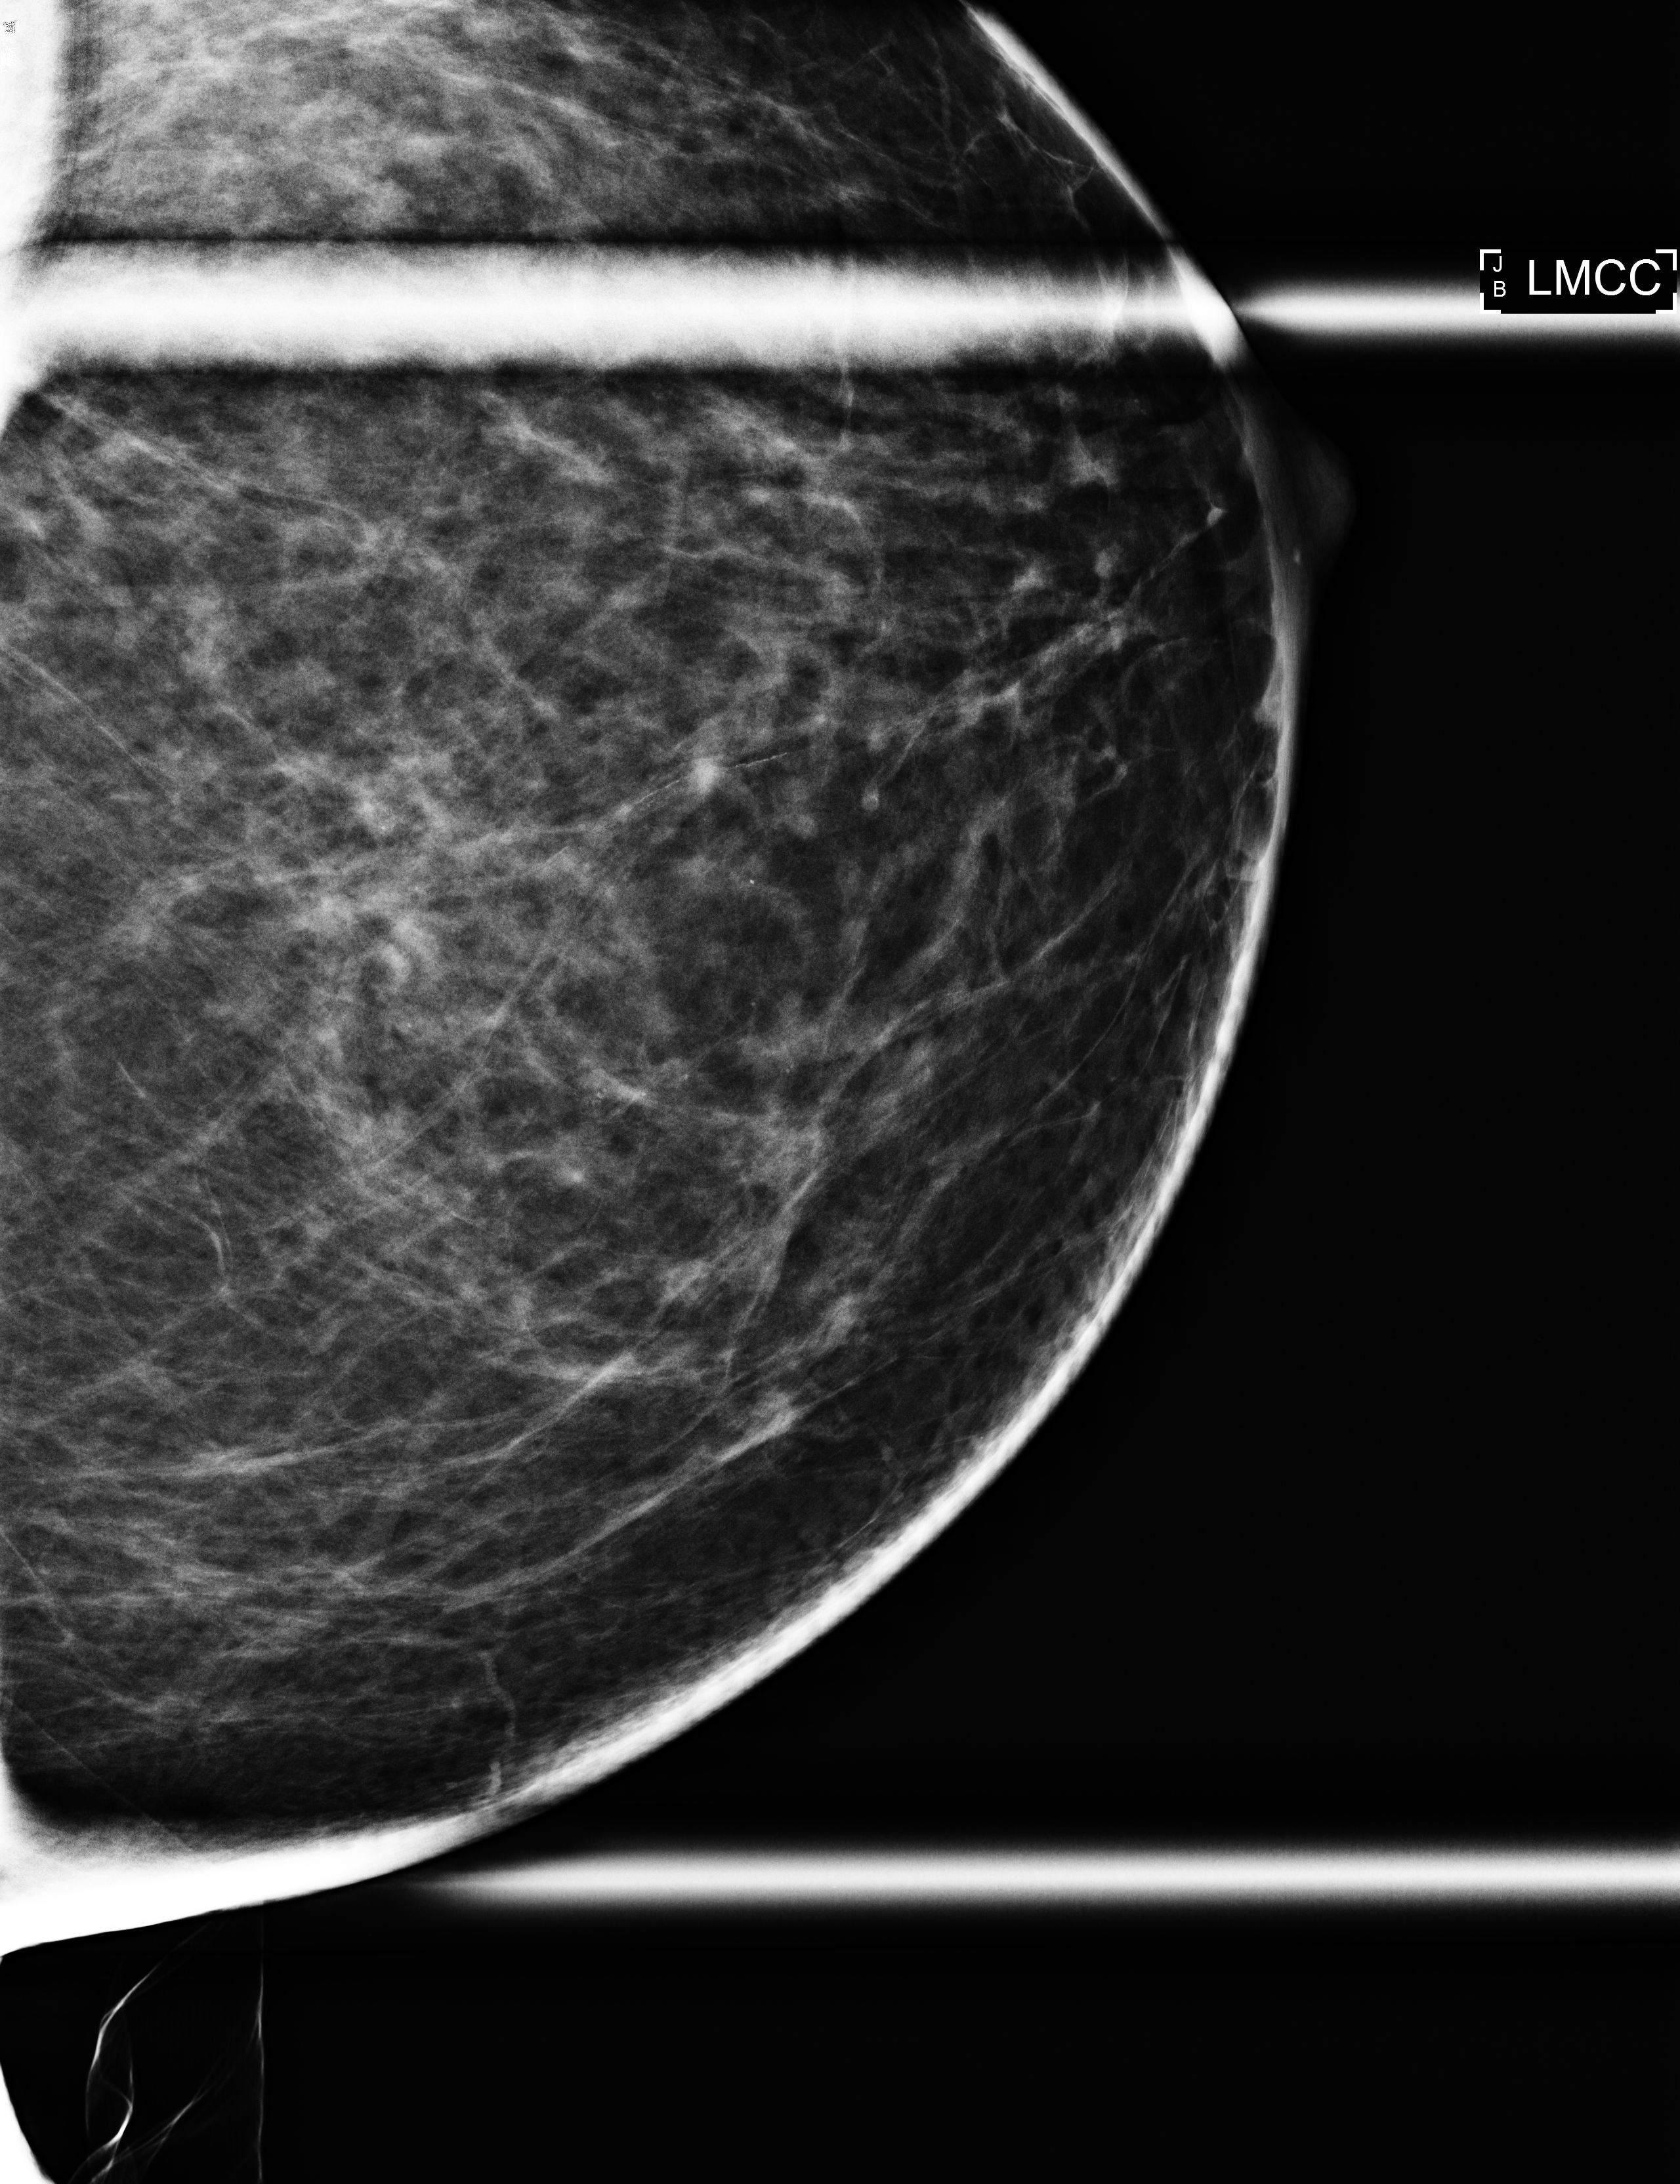
Full-field digital mammogram (FFDM), left breast, cranio-caudal projection (magnification), additional work-up view, compressed breast thickness 64 mm. Patient: female, 62 years.
BI-RADS breast density category at the screening exam (both breasts, scale 1–4): 2. Final BI-RADS category for the screening round (tomosynthesis exam, both breasts): category 2. Recall: recalled for additional imaging after this screen.